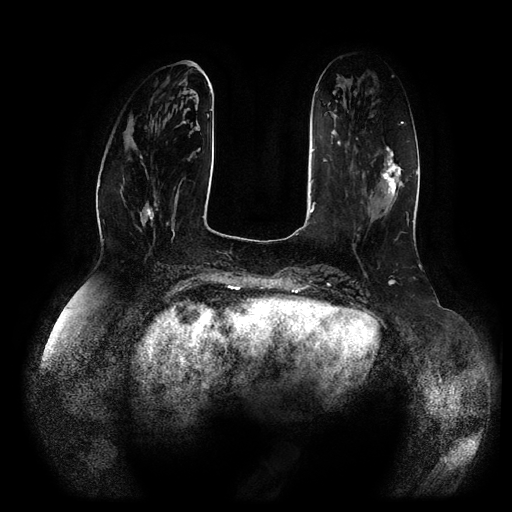
Breast MRI (dynamic contrast-enhanced, multi-phase), one axial slice. Slice 32 of 116 in the series (ordered by position). Dynamic contrast-enhanced series, time point 2 of 5 at this slice position (early post-contrast). 1.5 T. TE 2.5 ms, TR 5.2 ms. 2 mm slice thickness. 512 × 512 image matrix. Patient: female, 66 years.
Outlined on this slice (semi-automatic segmentation, software-assisted and operator-edited):
- breast lesion (labelled 'tumour' in the annotation; benign lesions carry a separate 'benign' label): bounding box <381,147,404,207> (left, top, right, bottom; pixels)